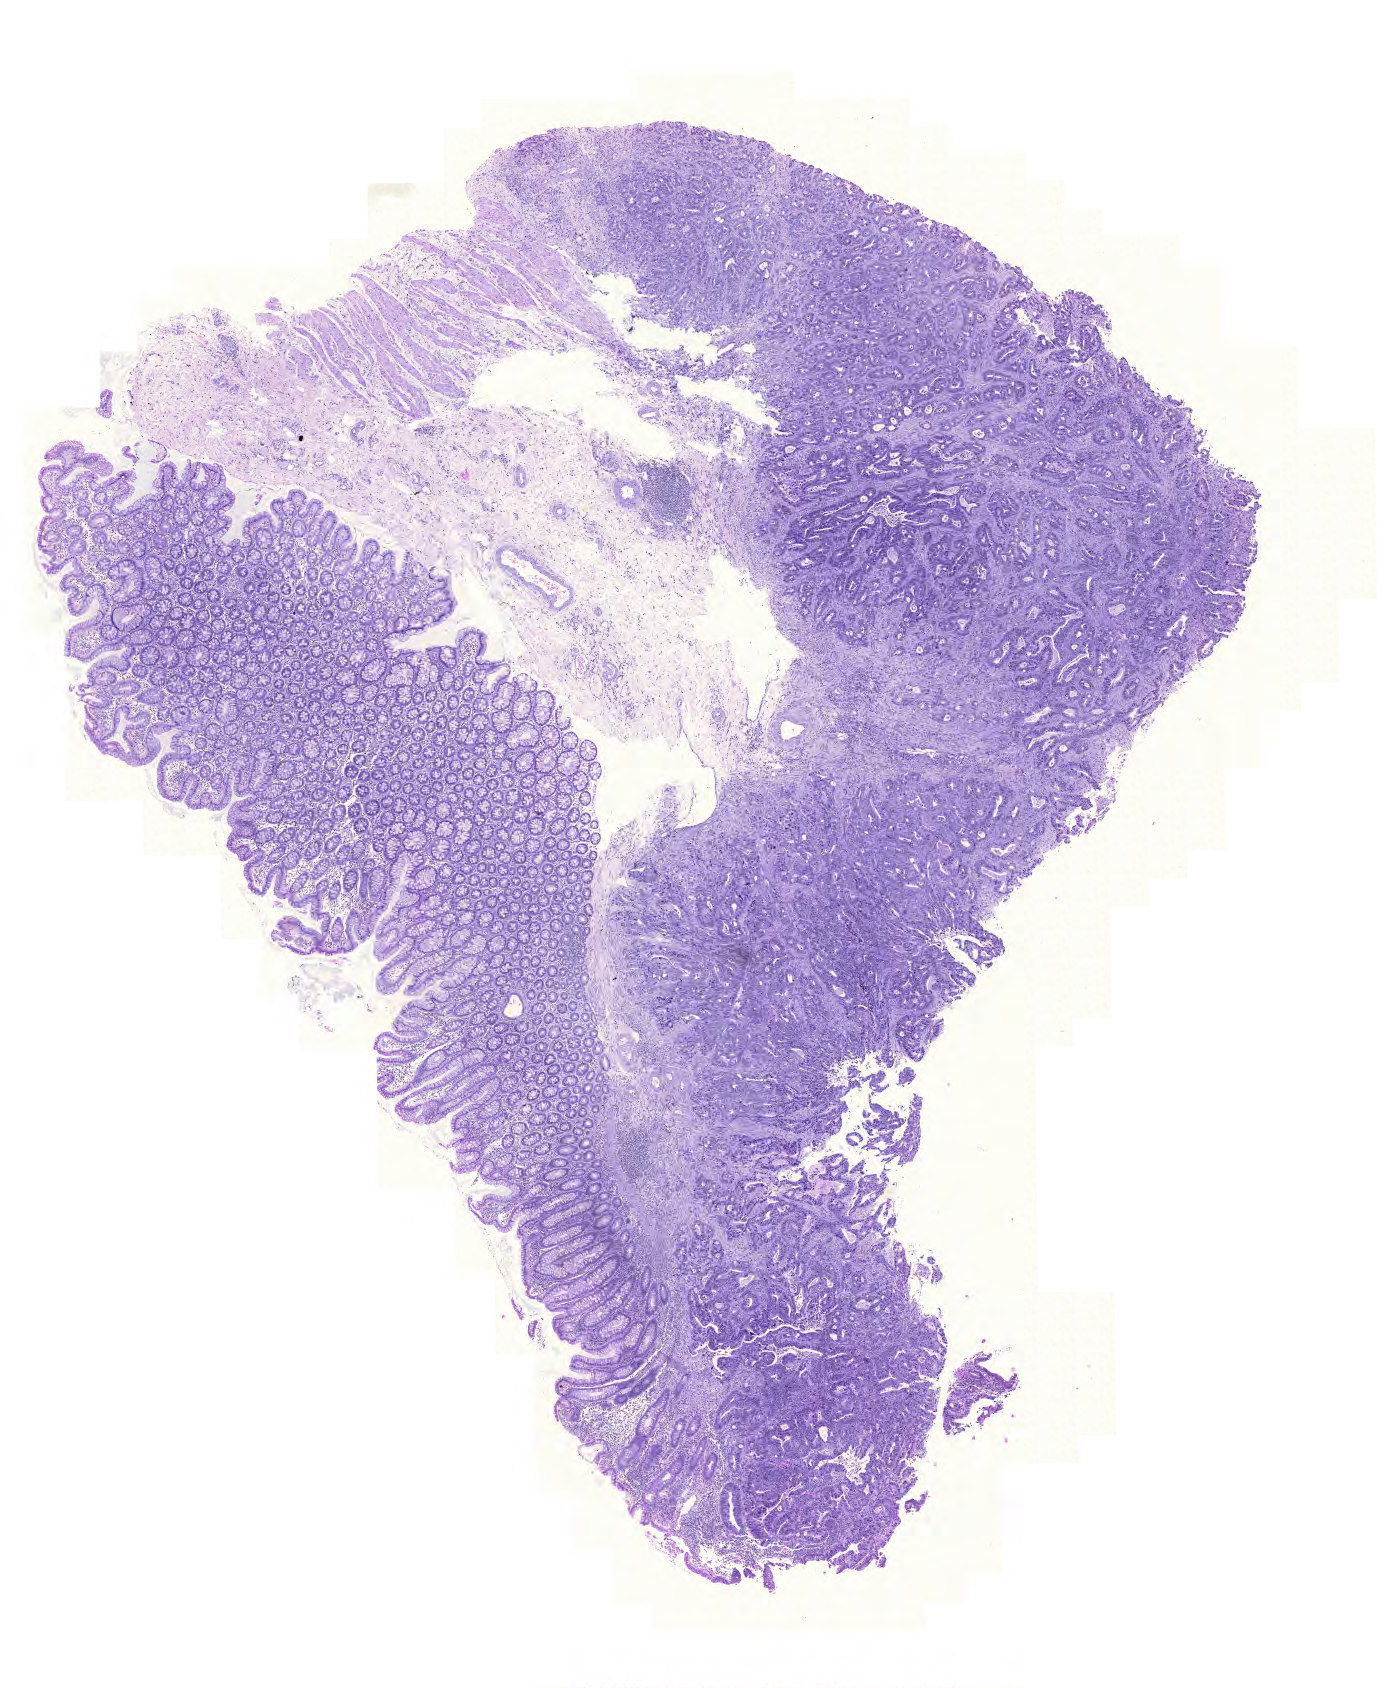
Whole-slide histology image, H&E, a low-resolution overview of the entire scanned area, about 10.3 x 12.6 mm (slide scanned at 20x), formalin-fixed paraffin-embedded (FFPE) diagnostic section, sample: primary tumour, colon. Male patient; age at initial diagnosis 69 years.
- AJCC pathologic stage: I (6th edition)
- histologic diagnosis: Adenocarcinoma, NOS